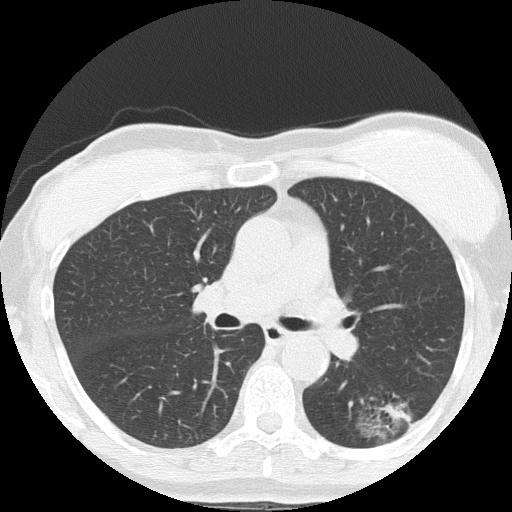
Low-dose screening chest CT, axial slice. Third screening round (two years after baseline). Lung window (W 1500 / L -600 HU). 2 mm slice thickness. Slice 62 of 152 in the series. Female, age 64 years at enrolment. Former smoker at enrolment.
Expert-annotated lung lesion, box from (x=353, y=379) to (x=441, y=450) px. The screening reader recorded 3 non-calcified nodules or masses ≥4 mm on this exam (right upper lobe, left lower lobe, right middle lobe); which of them this box marks is not recorded. Participant outcome: lung cancer diagnosed 212 days after this screen — adenocarcinoma, NOS, left lower lobe, moderately differentiated (G2), stage IA (AJCC 6th edition), 17 mm at pathology.